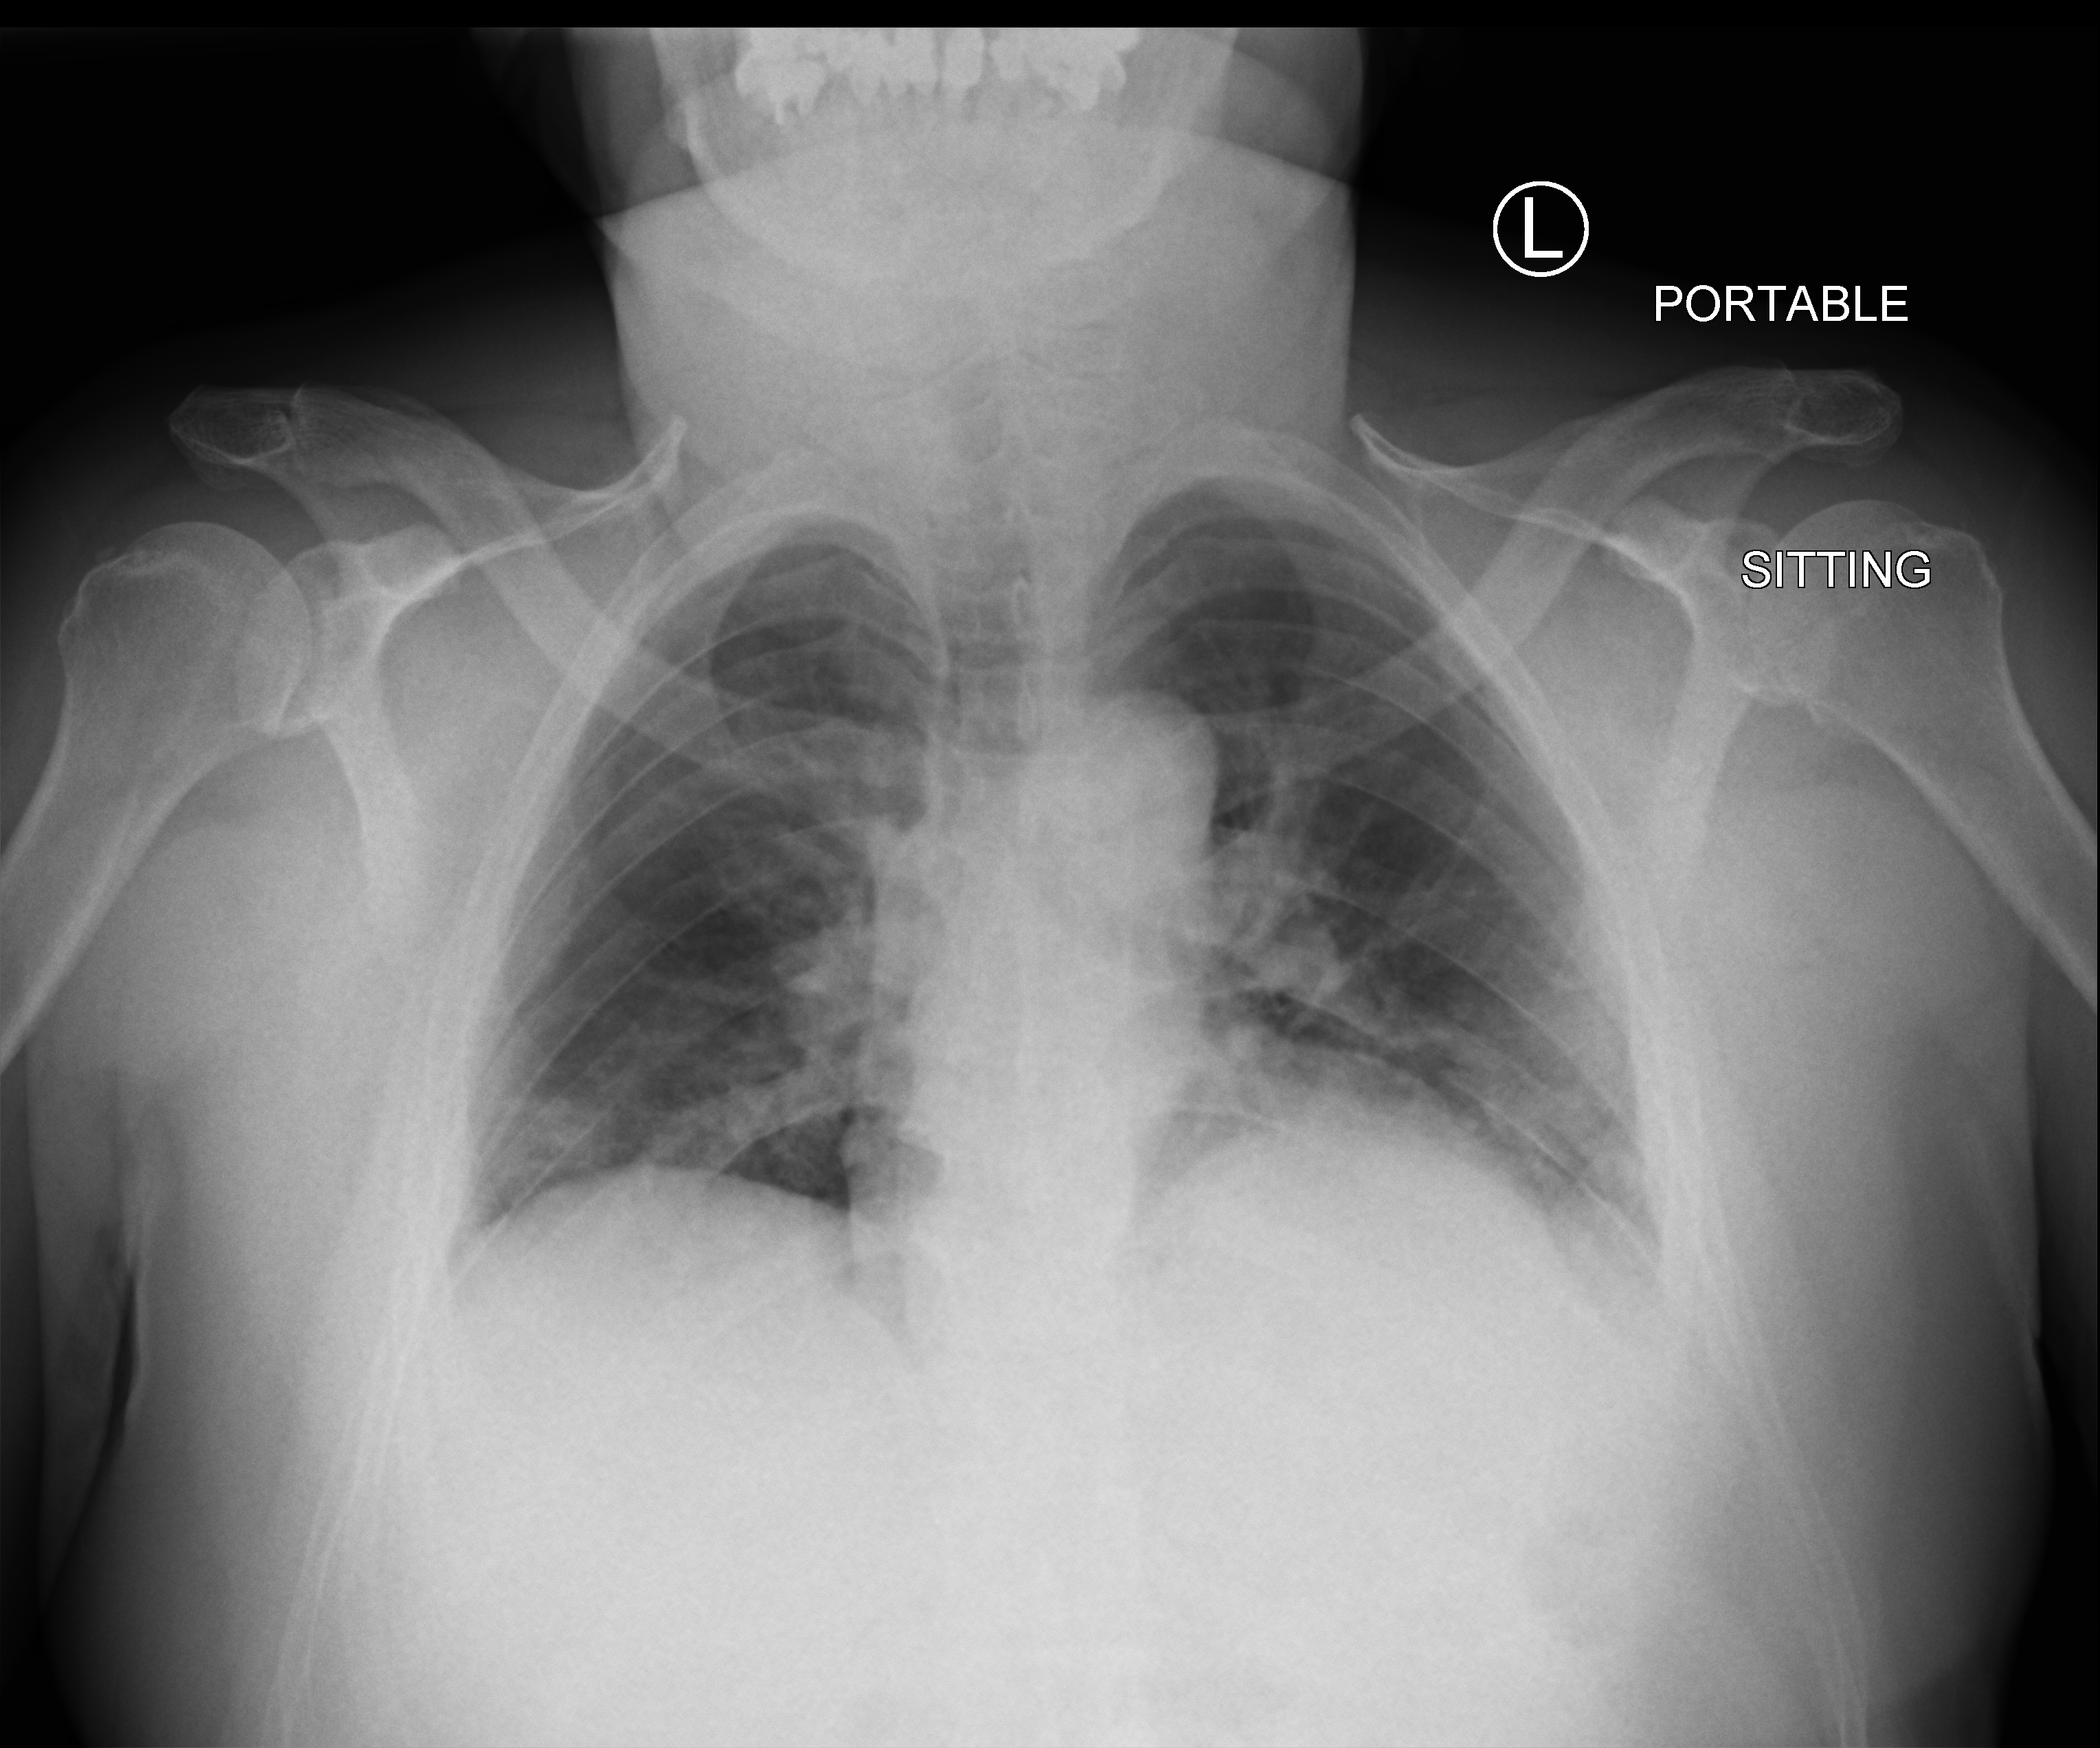
Bedside chest radiograph (computed radiography); anteroposterior (AP) projection. Patient hospitalised with COVID-19; male, aged 60–74 years.
Admission-level facts for this patient (not findings on this image; timing relative to this image not recorded): admitted to intensive care during this hospital stay: no; diabetes (admission record): no; other chronic lung disease (admission record): no.